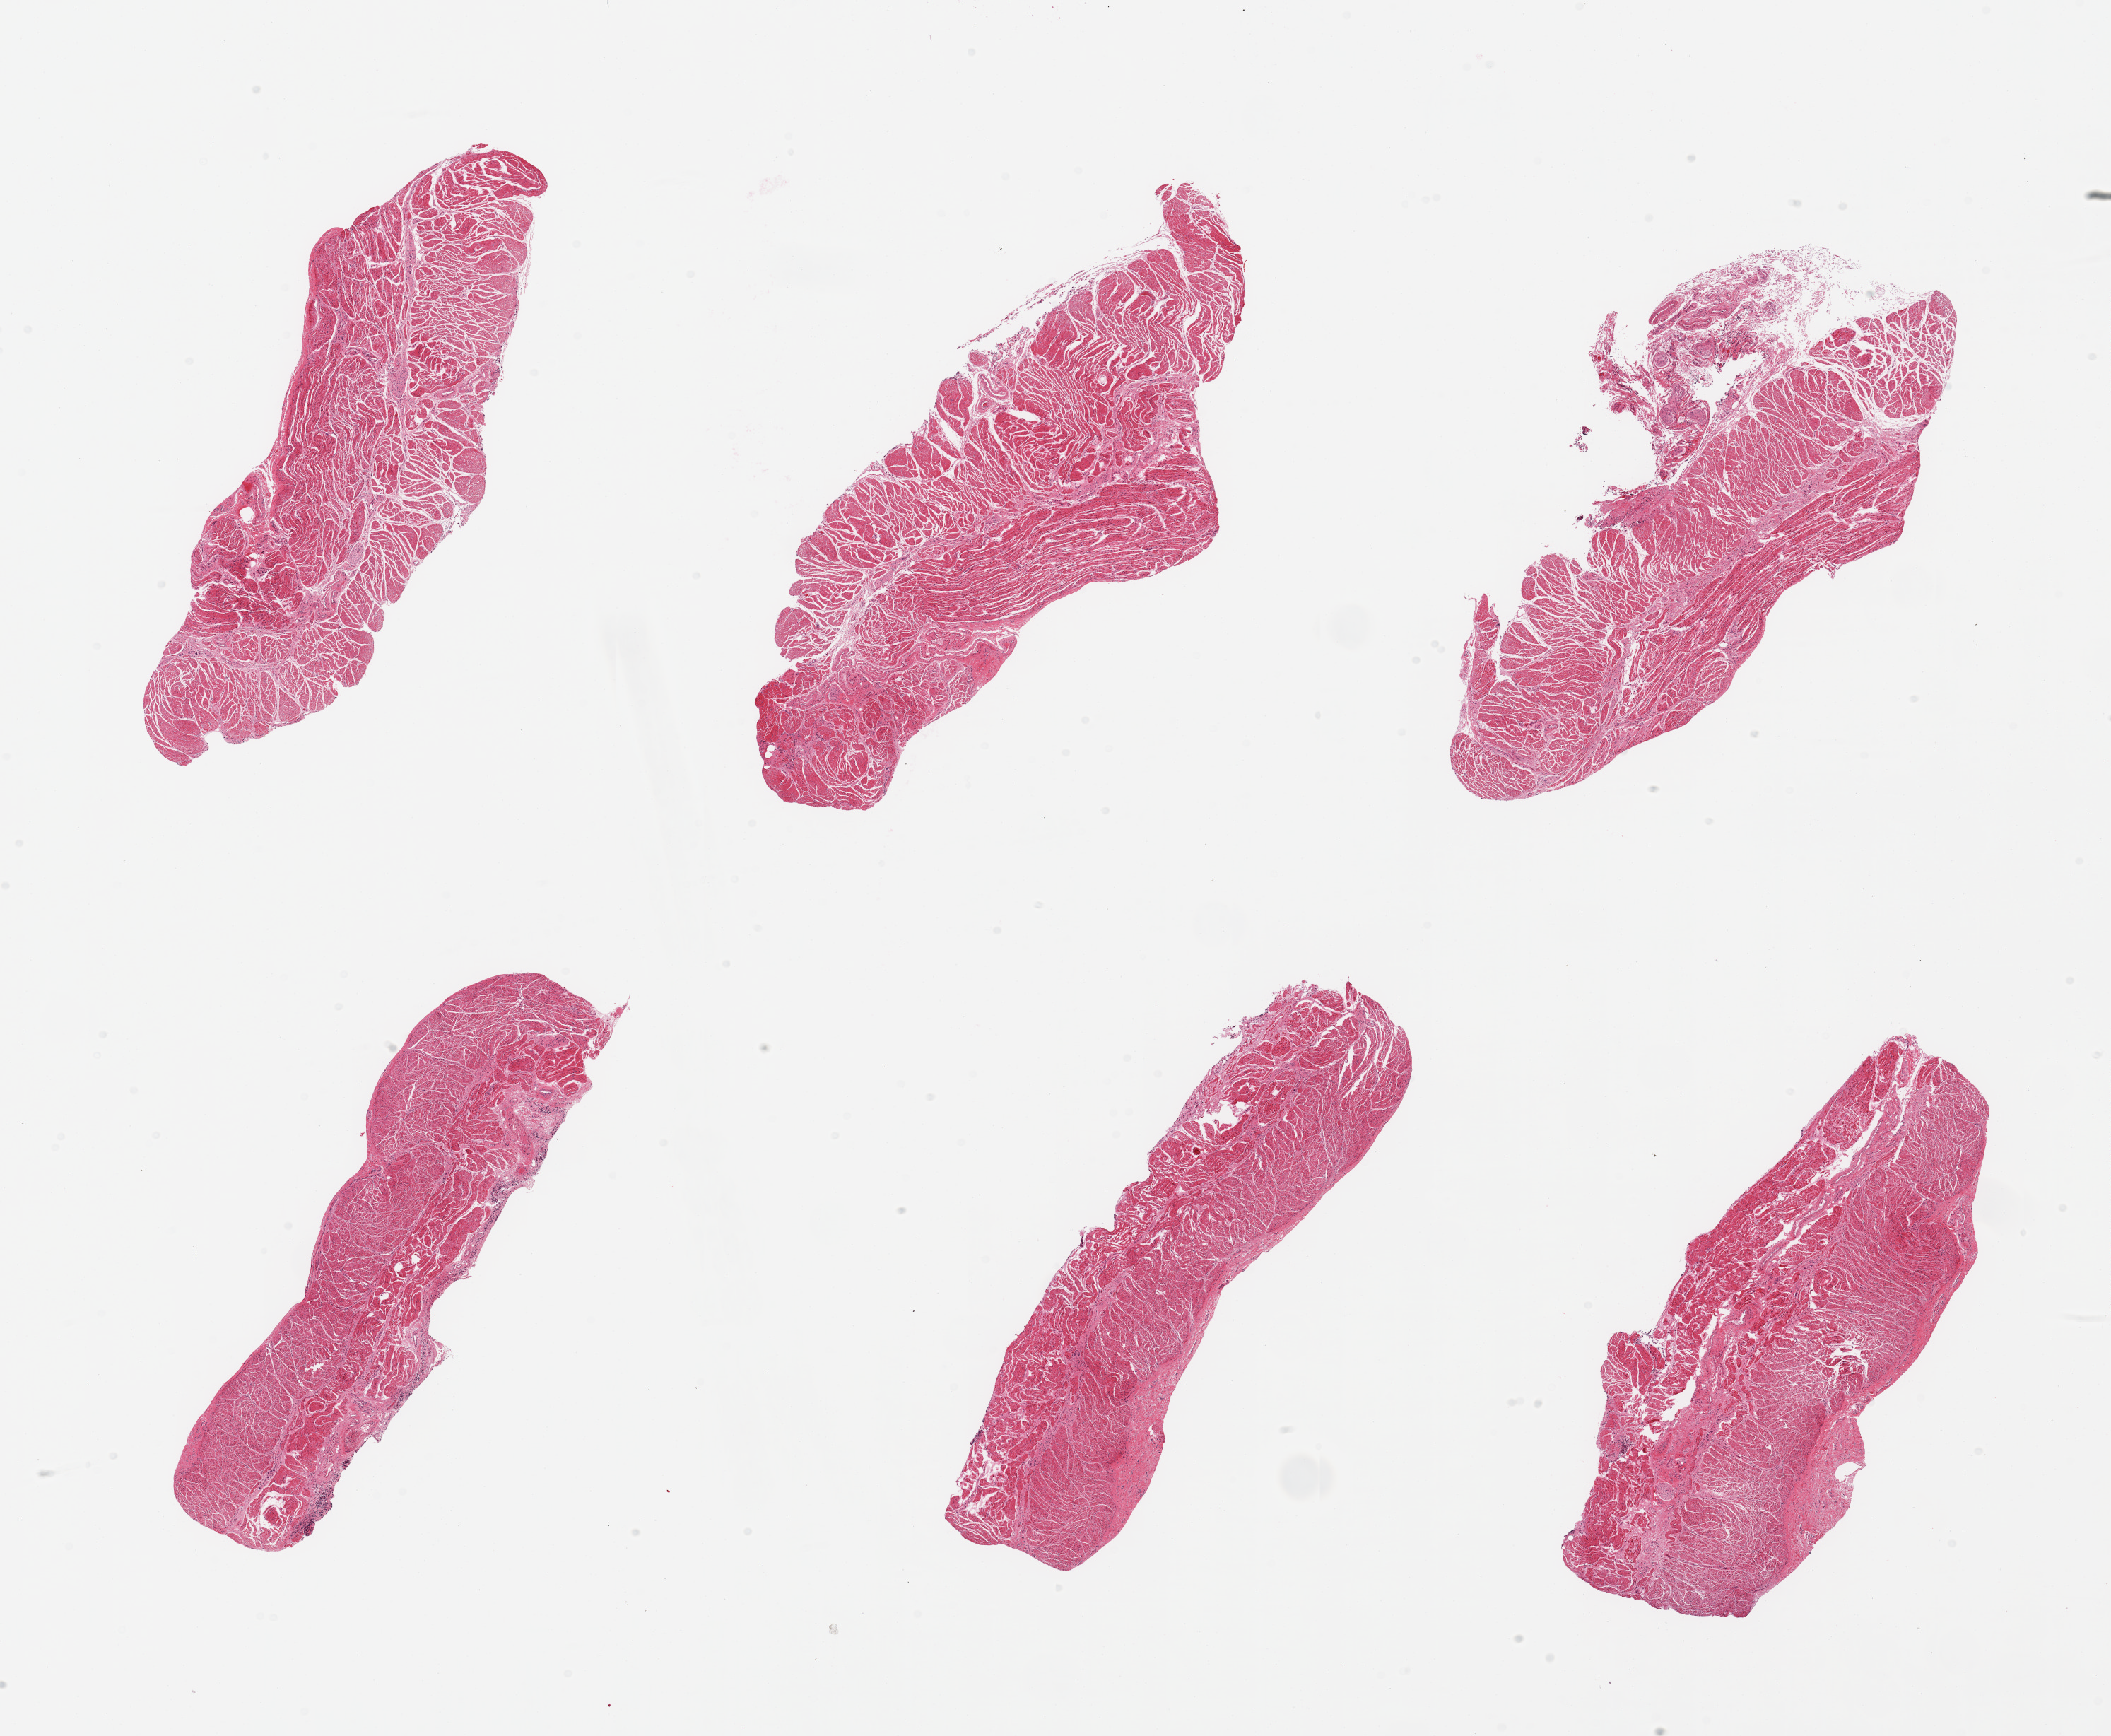
H&E whole-slide image — shown as a low-resolution overview of the whole scanned area (about 23.6 x 19.4 mm, from a 20x scan); PAXgene-fixed paraffin-embedded (PFPE) section; section of esophageal muscle (target tissue); donor tissue sample. Donor sex: female.
* reviewer comment on this tissue sample: 6 pieces; well trimmed muscularis